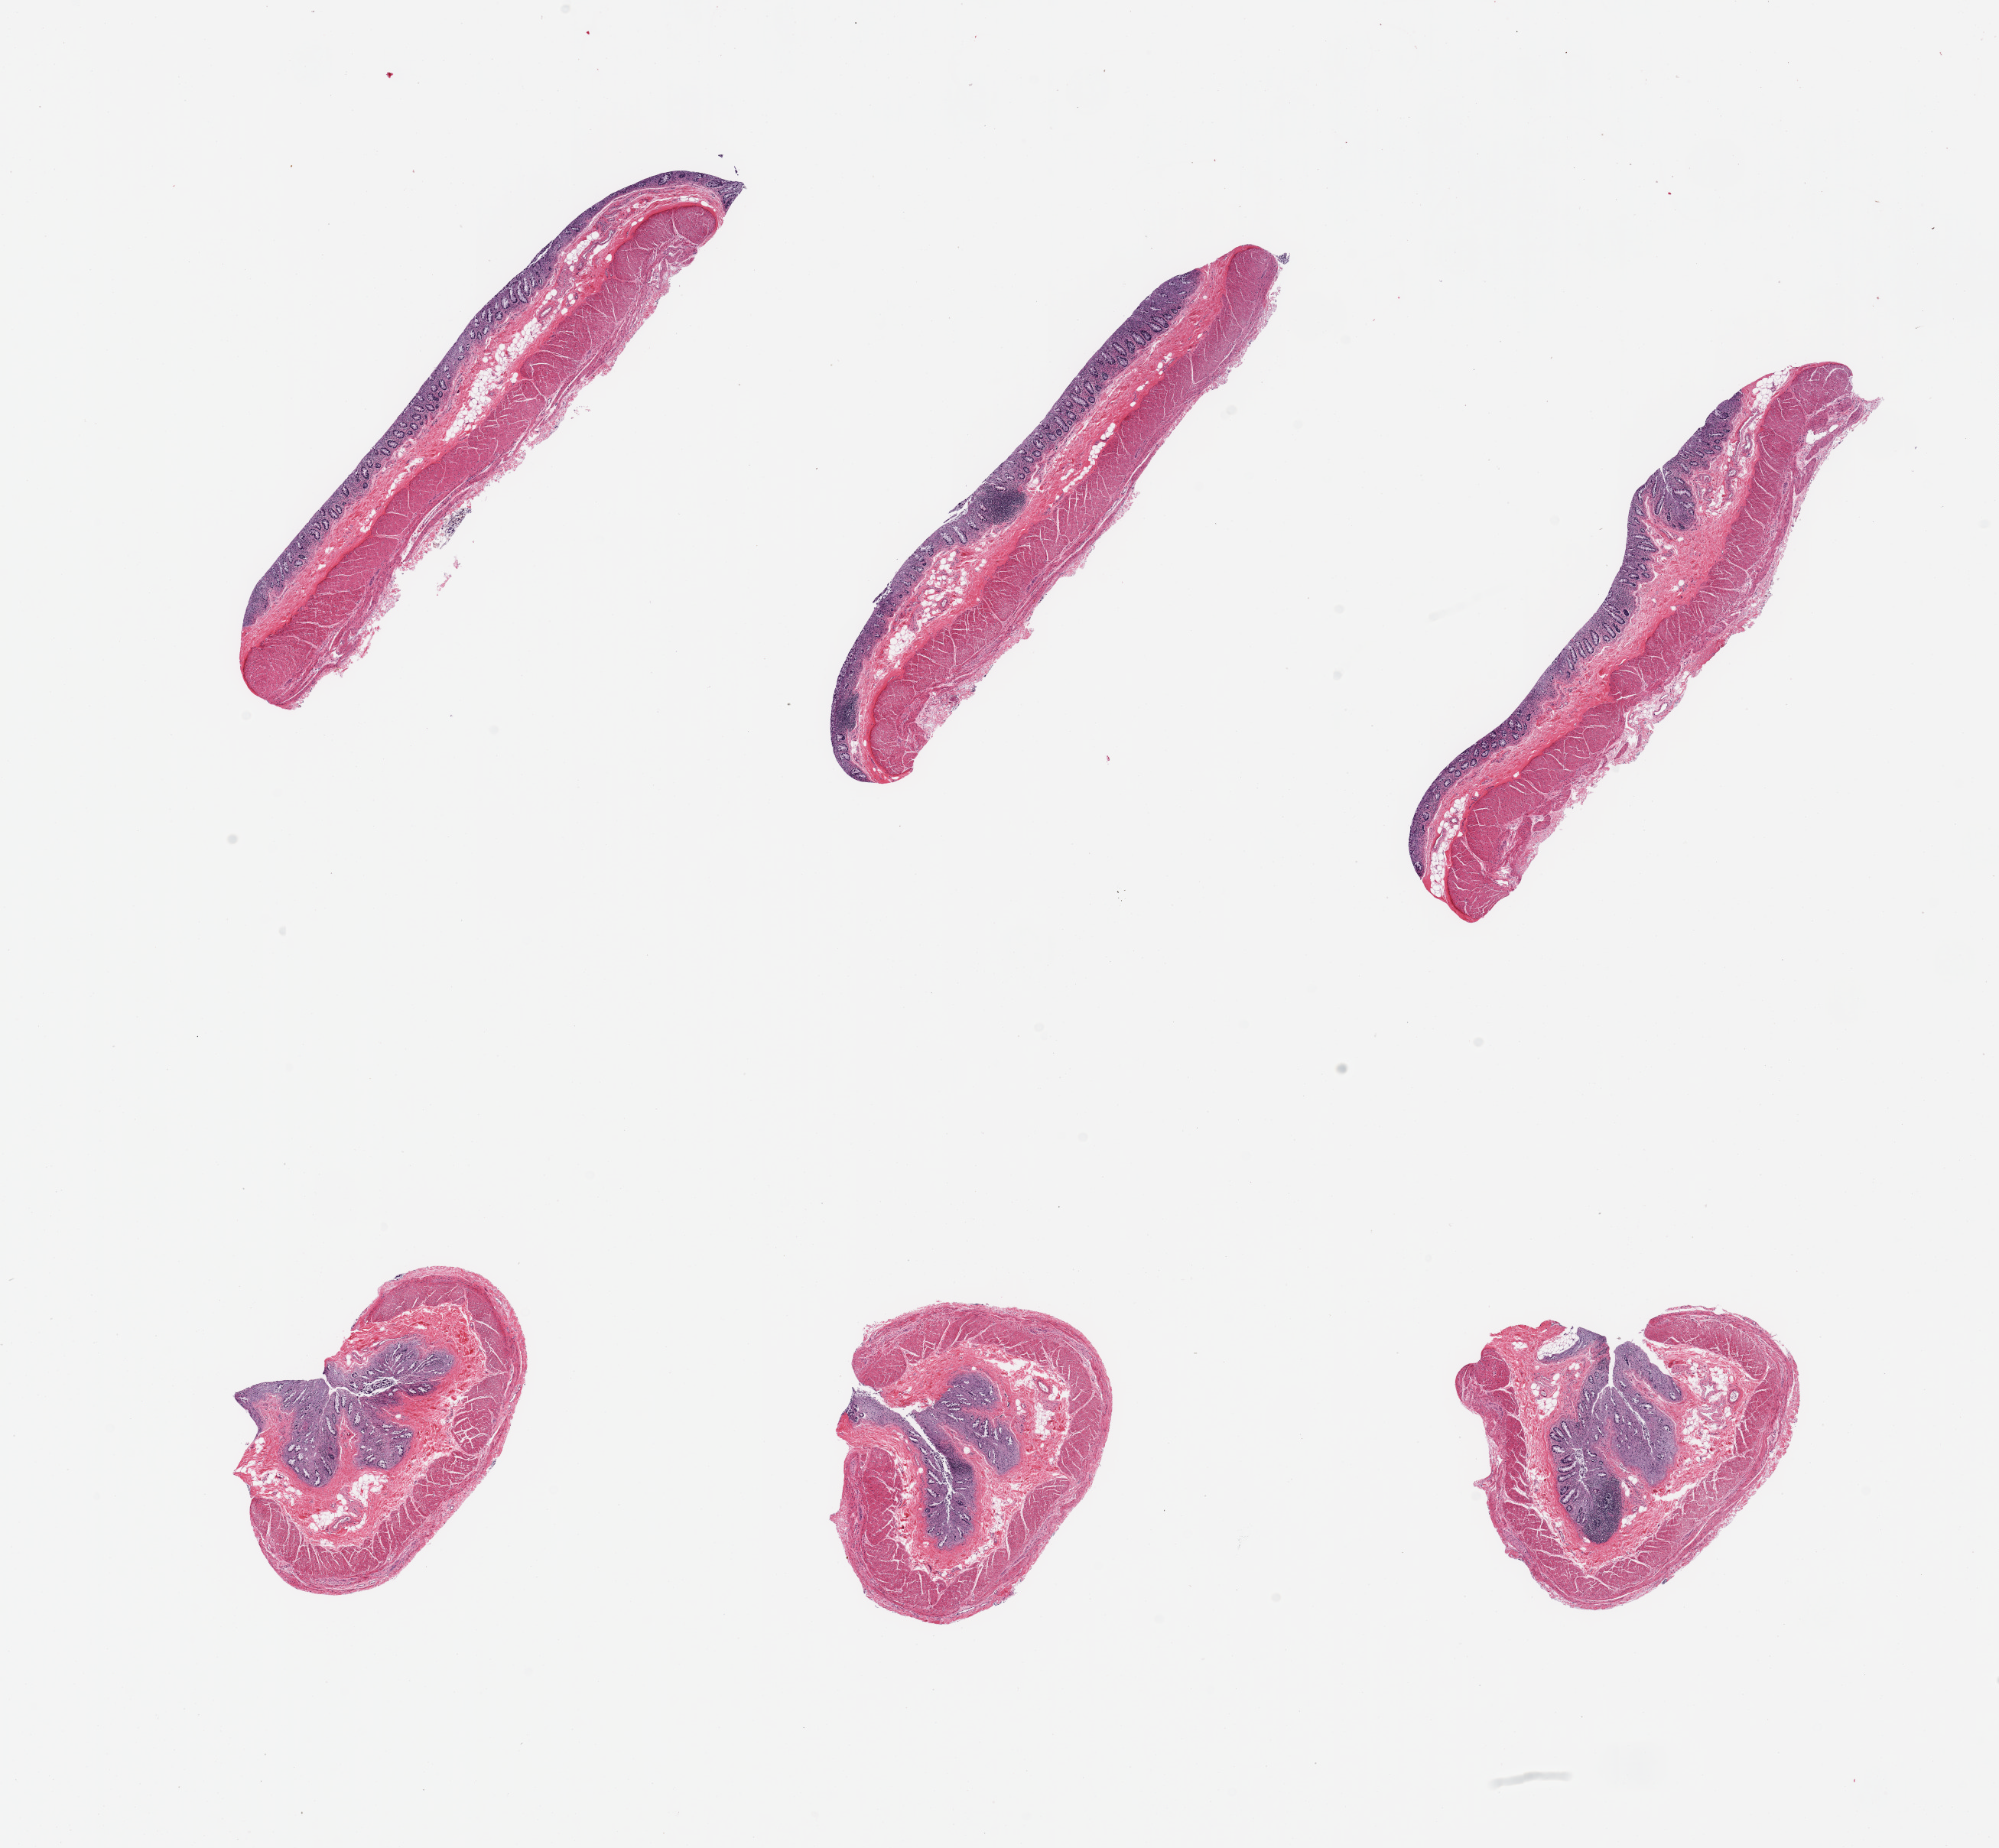
Whole-slide image, hematoxylin and eosin (H&E) stain — low-resolution overview of the scanned area, about 20.7 x 19.1 mm. PAXgene-fixed paraffin-embedded (PFPE) section. Target tissue: transverse colon. Donor tissue sample. Donor: male.
* review note (as recorded): 6 pieces; mucosa moderately autolyzed, muscularis intact